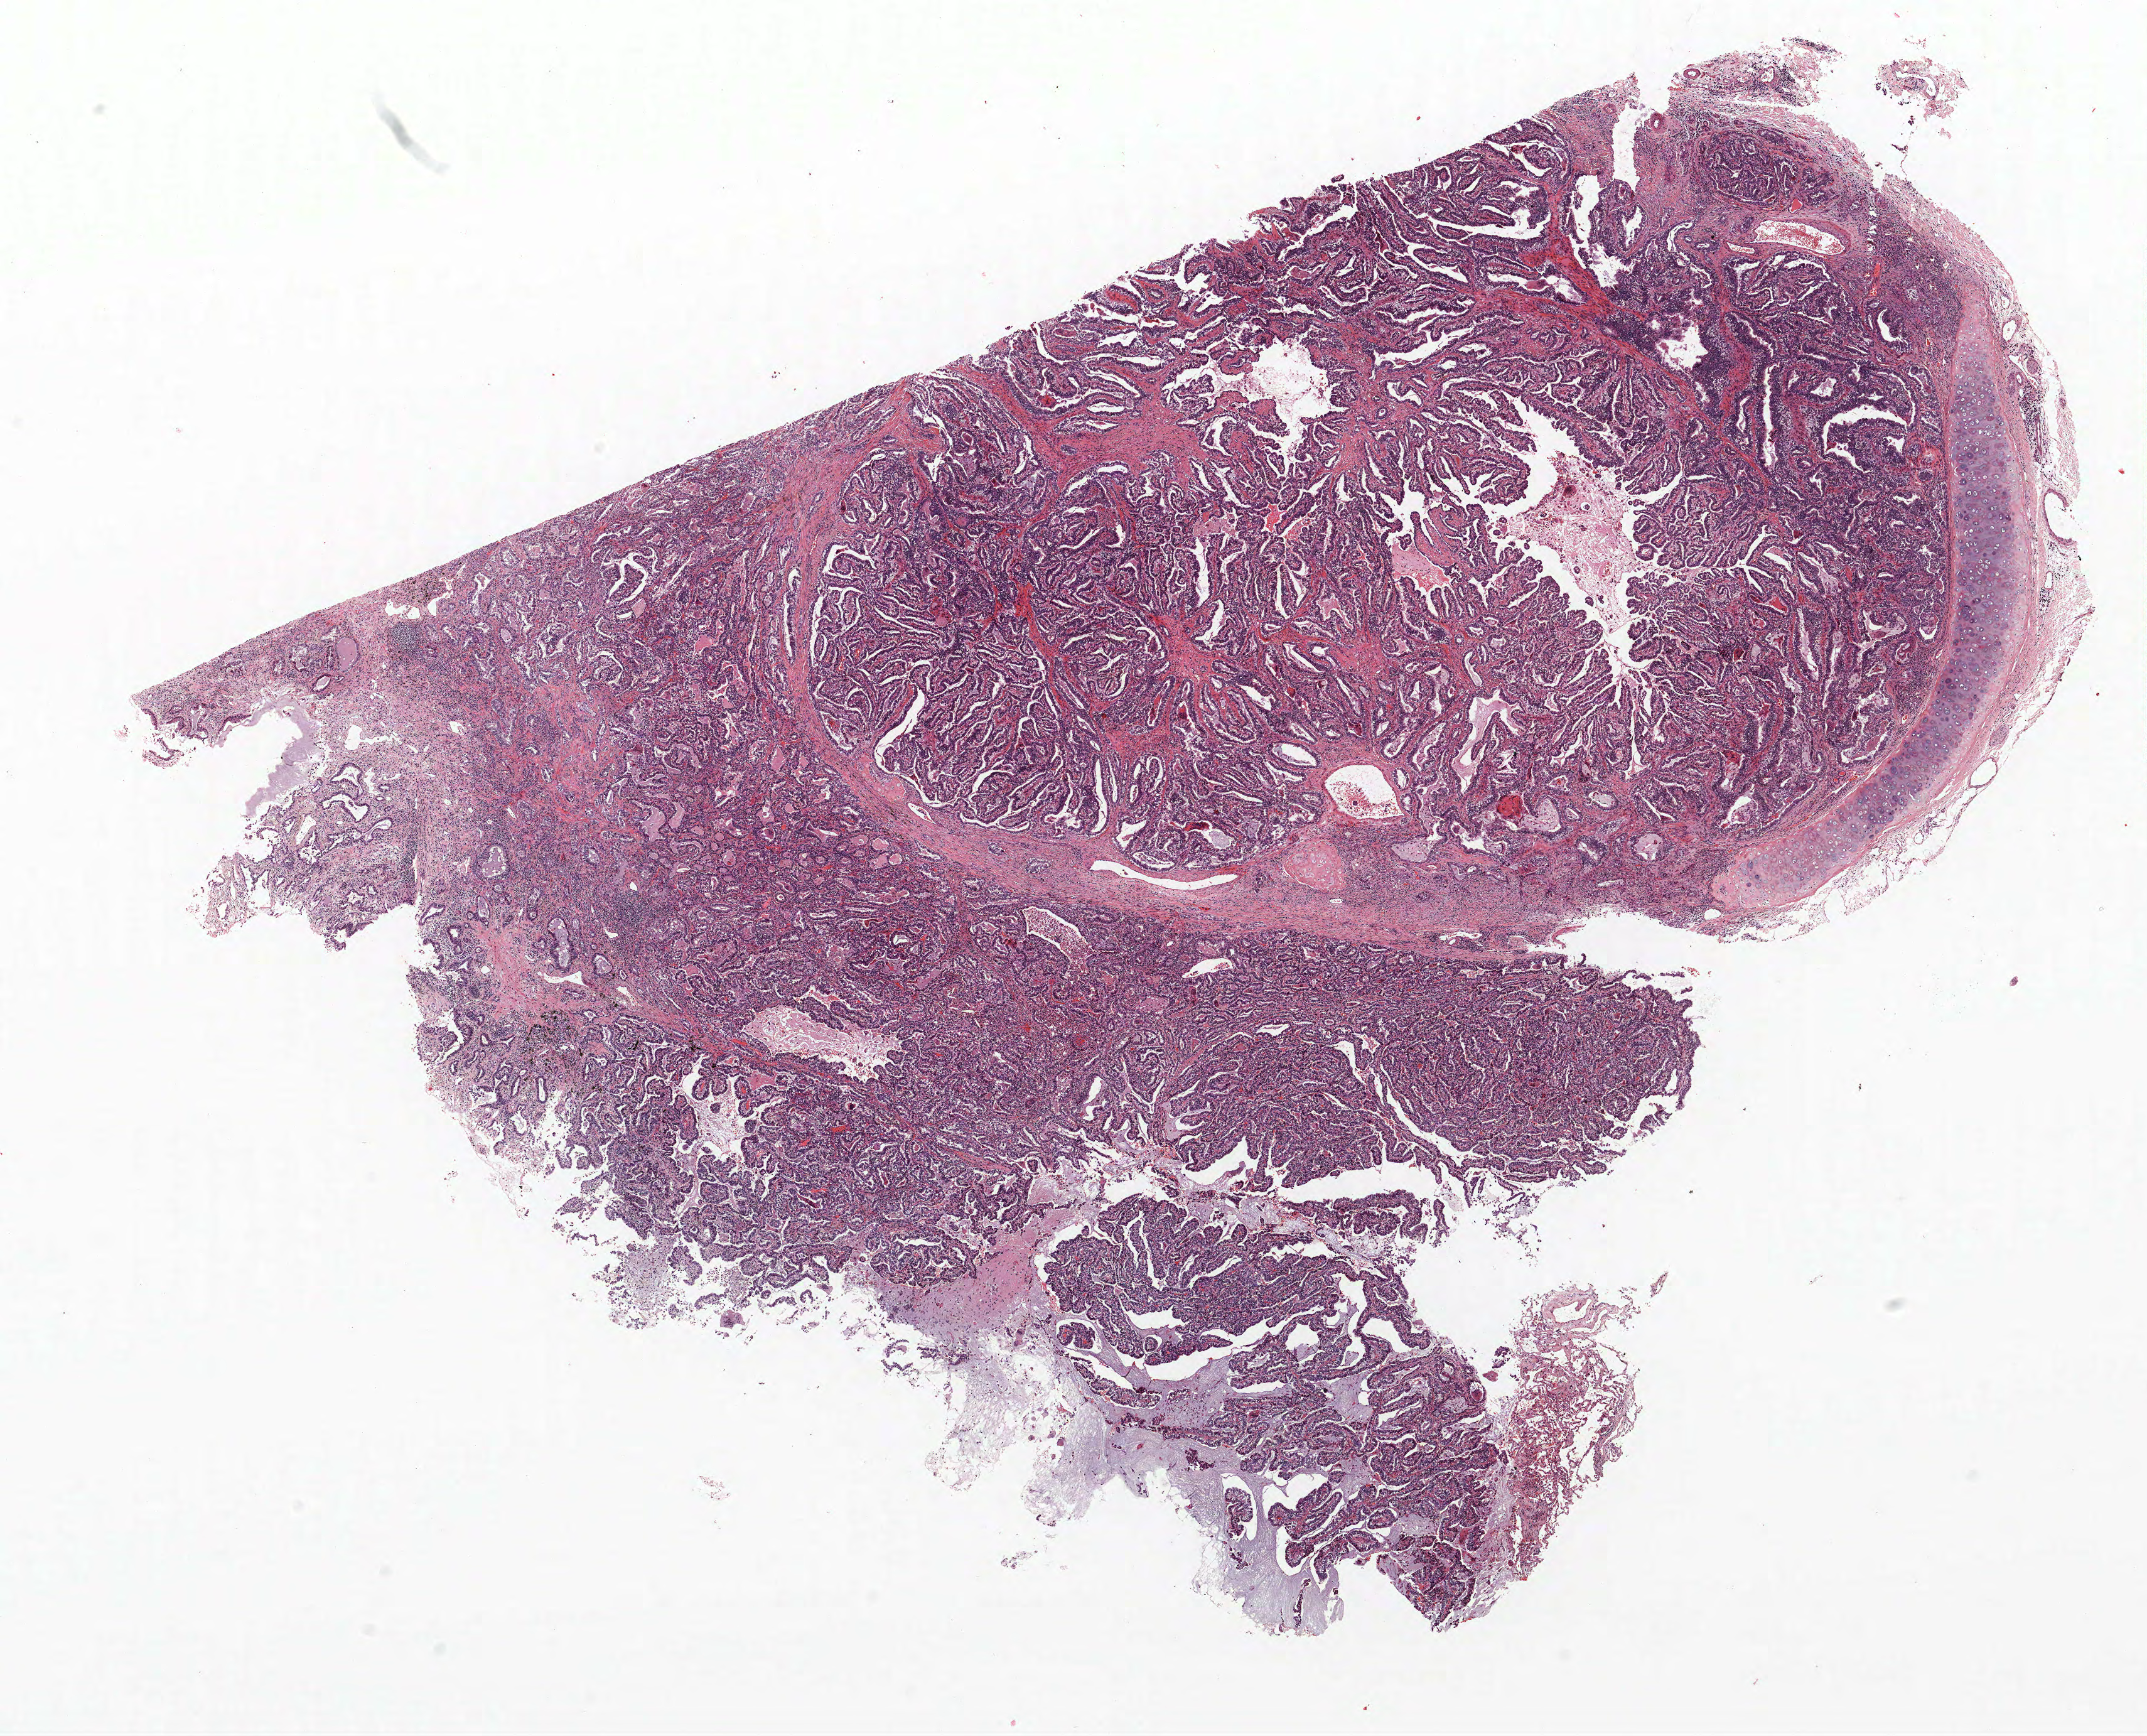
Whole-slide histology image, H&E, shown as a low-resolution overview of the whole scanned area (about 13.7 x 11.1 mm), FFPE section, lung tissue. Male, age 58 at enrolment. Current smoker at enrolment. Grade: well differentiated (G1).
Tumour size (pathology): 17 mm. Primary tumour location (clinical record): left upper lobe. Participant's lung-cancer diagnosis: Bronchiolo-alveolar adenocarcinoma, NOS (ICD-O-3 8250/3). Stage (AJCC 6th edition): IA. ICD-O-3 topography: upper lobe of lung (C34.1).